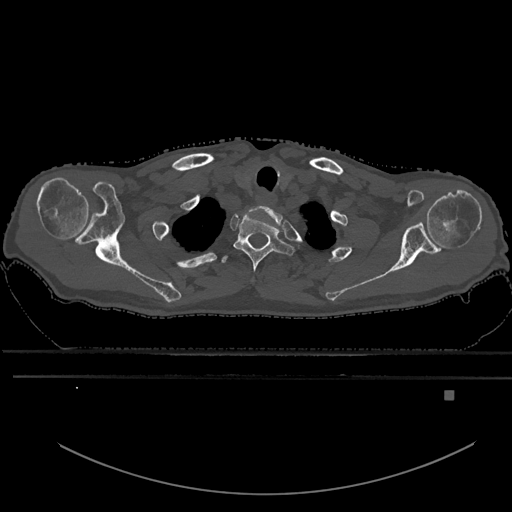
CT including the spine, one axial slice. Slice 537 of 969 in the series (ordered by position). Bone window (W 1800 / L 400 HU). 0.5 mm slice thickness. 512 × 512 image matrix, field of view 456 × 456 mm. Male patient, age 82 years. Case-level facts recorded for this patient, not image findings: primary cancer: prostate.
Structures marked on this image (semi-automatically segmented with operator editing):
- T1 vertebra: bounding box <233,212,294,272> (left, top, right, bottom; pixels)
- T2 vertebra: <221,255,229,264>